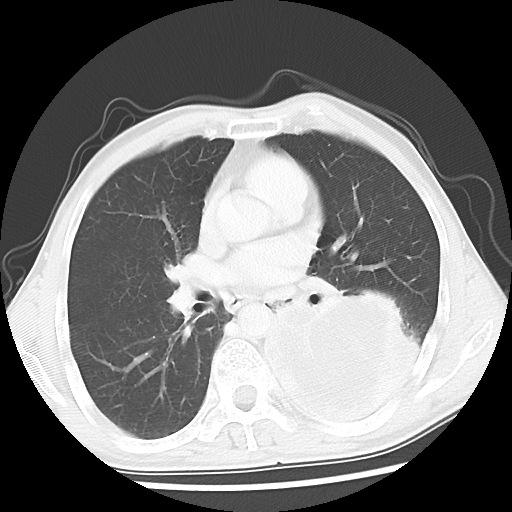
Chest CT, one axial slice. Slice 26 of 52 in the series (ordered by position). Reconstruction kernel LUNG. Lung window (W 1500 / L -600 HU). 5 mm slice thickness. 512 × 512 image matrix, field of view 318 × 318 mm. Male patient, age 60 years. From the clinical record (not read from this slice): clinical TNM (as recorded): T4 N0 M0.
Annotated regions visible in this slice (bounding box drawn by a radiologist):
- lung tumour (recorded histology: squamous cell carcinoma): bounding box (x1, y1, x2, y2) in pixels: (251, 281, 430, 435)